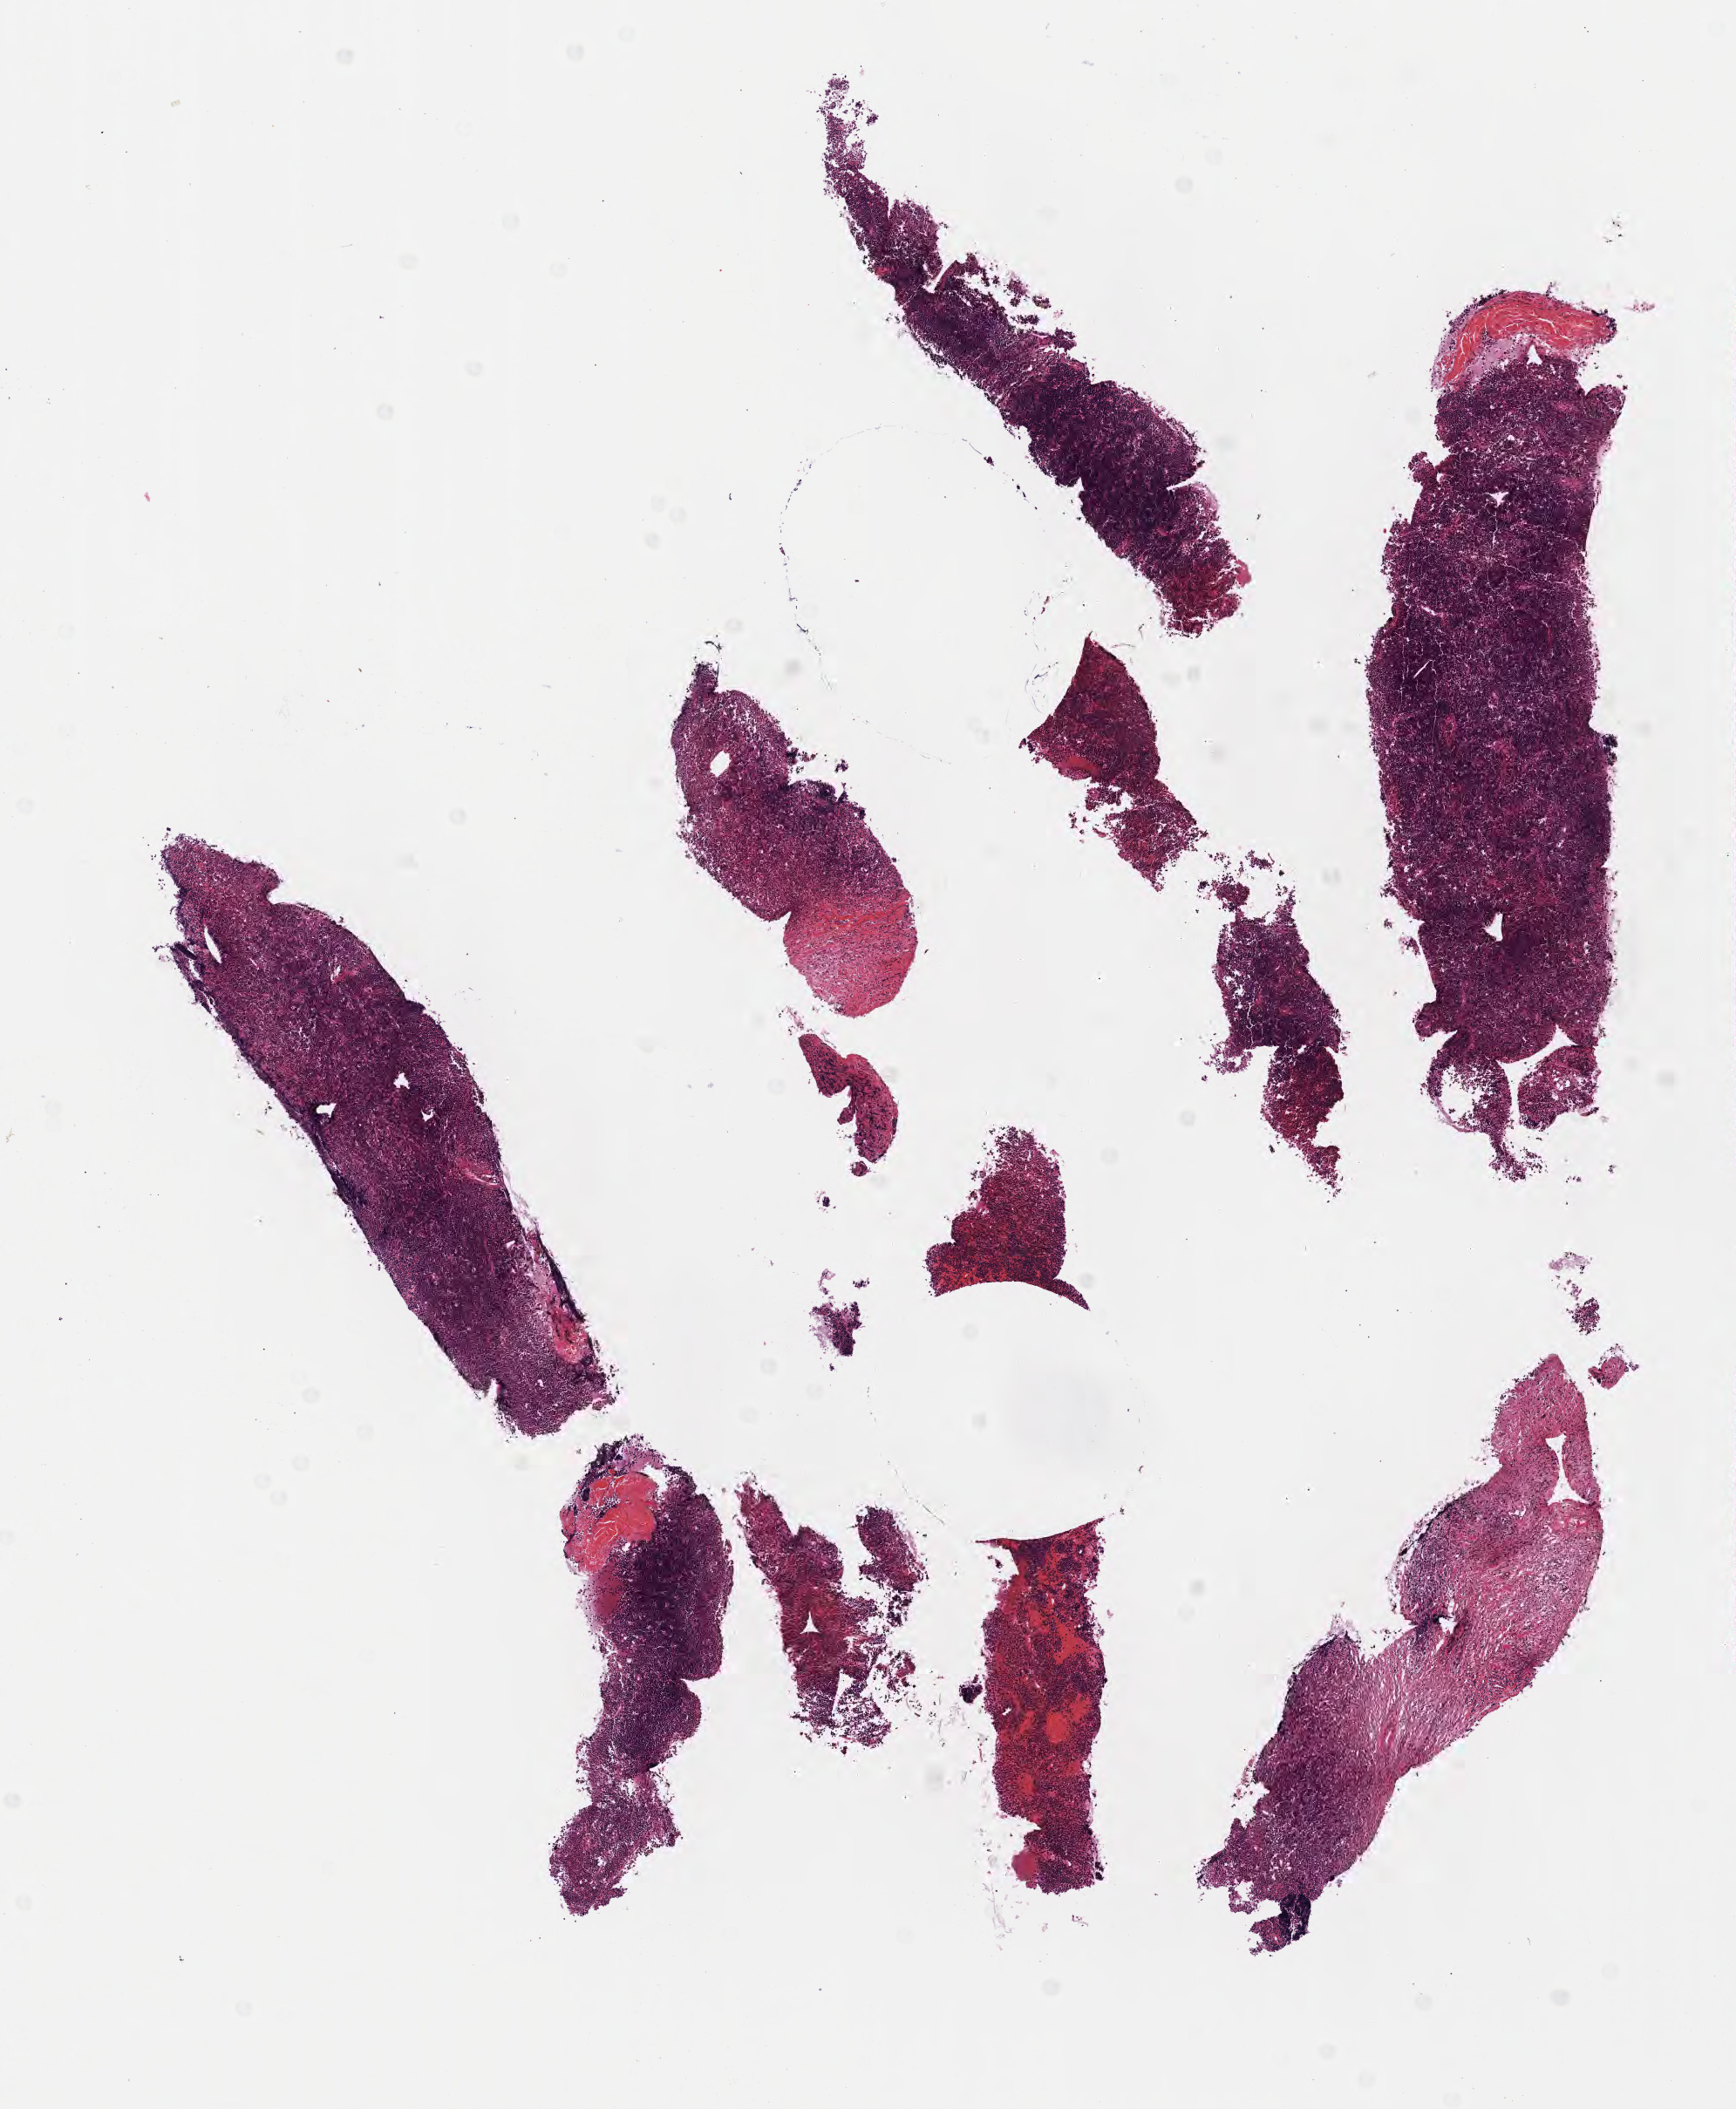
Hematoxylin and eosin (H&E) whole-slide image, a low-resolution overview of the entire scanned area, about 8.1 x 9.8 mm, specimen: tumor tissue, anatomic site: abdomen proper. Male patient; age at initial diagnosis 7 years.
Histologic diagnosis: Burkitt lymphoma, NOS.